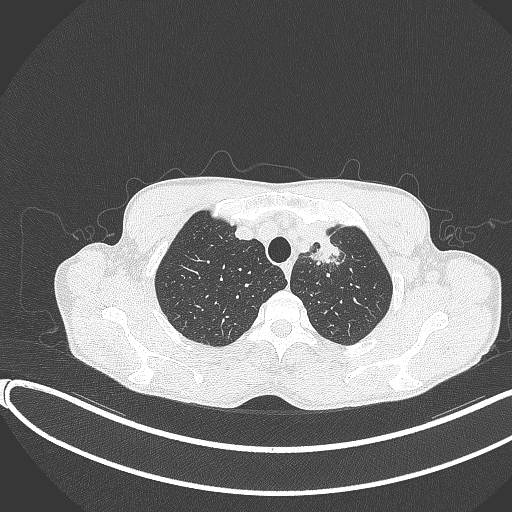
Chest CT, one axial slice. Position 328 of 374 along the scan axis. Reconstruction kernel B70f. 120 kVp. Lung window (W 1500 / L -600 HU). 512 × 512 image matrix, field of view 400 × 400 mm. Patient: male, 58 years. Case-level facts recorded for this patient, not image findings: clinical TNM (as recorded): T1c N1 M0.
Outlined on this slice (bounding box drawn by a radiologist):
- lung tumour (recorded histology: adenocarcinoma): box from (x=304, y=224) to (x=348, y=265) px